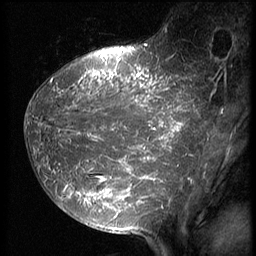
Breast MRI (dynamic contrast-enhanced), one sagittal slice. Position 21 of 64 along the scan axis. 3 images stored at this slice position (order not interpretable as contrast timing). 1.5 T. TE 4.2 ms, TR 9 ms. 256 × 256 image matrix, field of view 180 × 180 mm. Patient: female, 39 years. Case-level facts recorded for this patient, not image findings: setting: breast cancer imaged before/during neoadjuvant chemotherapy; receptor status: HER2-positive.
Annotated regions visible in this slice (semi-automatic segmentation, software-assisted and operator-edited):
- analysis volume of interest (the breast-tissue region the enhancement analysis was run in; not a lesion): bounding box [x1, y1, x2, y2] px = [24, 47, 210, 239]
- tumour enhancement mask (voxels above the 140 % enhancement threshold inside the analysis volume of interest): [26, 50, 210, 218]